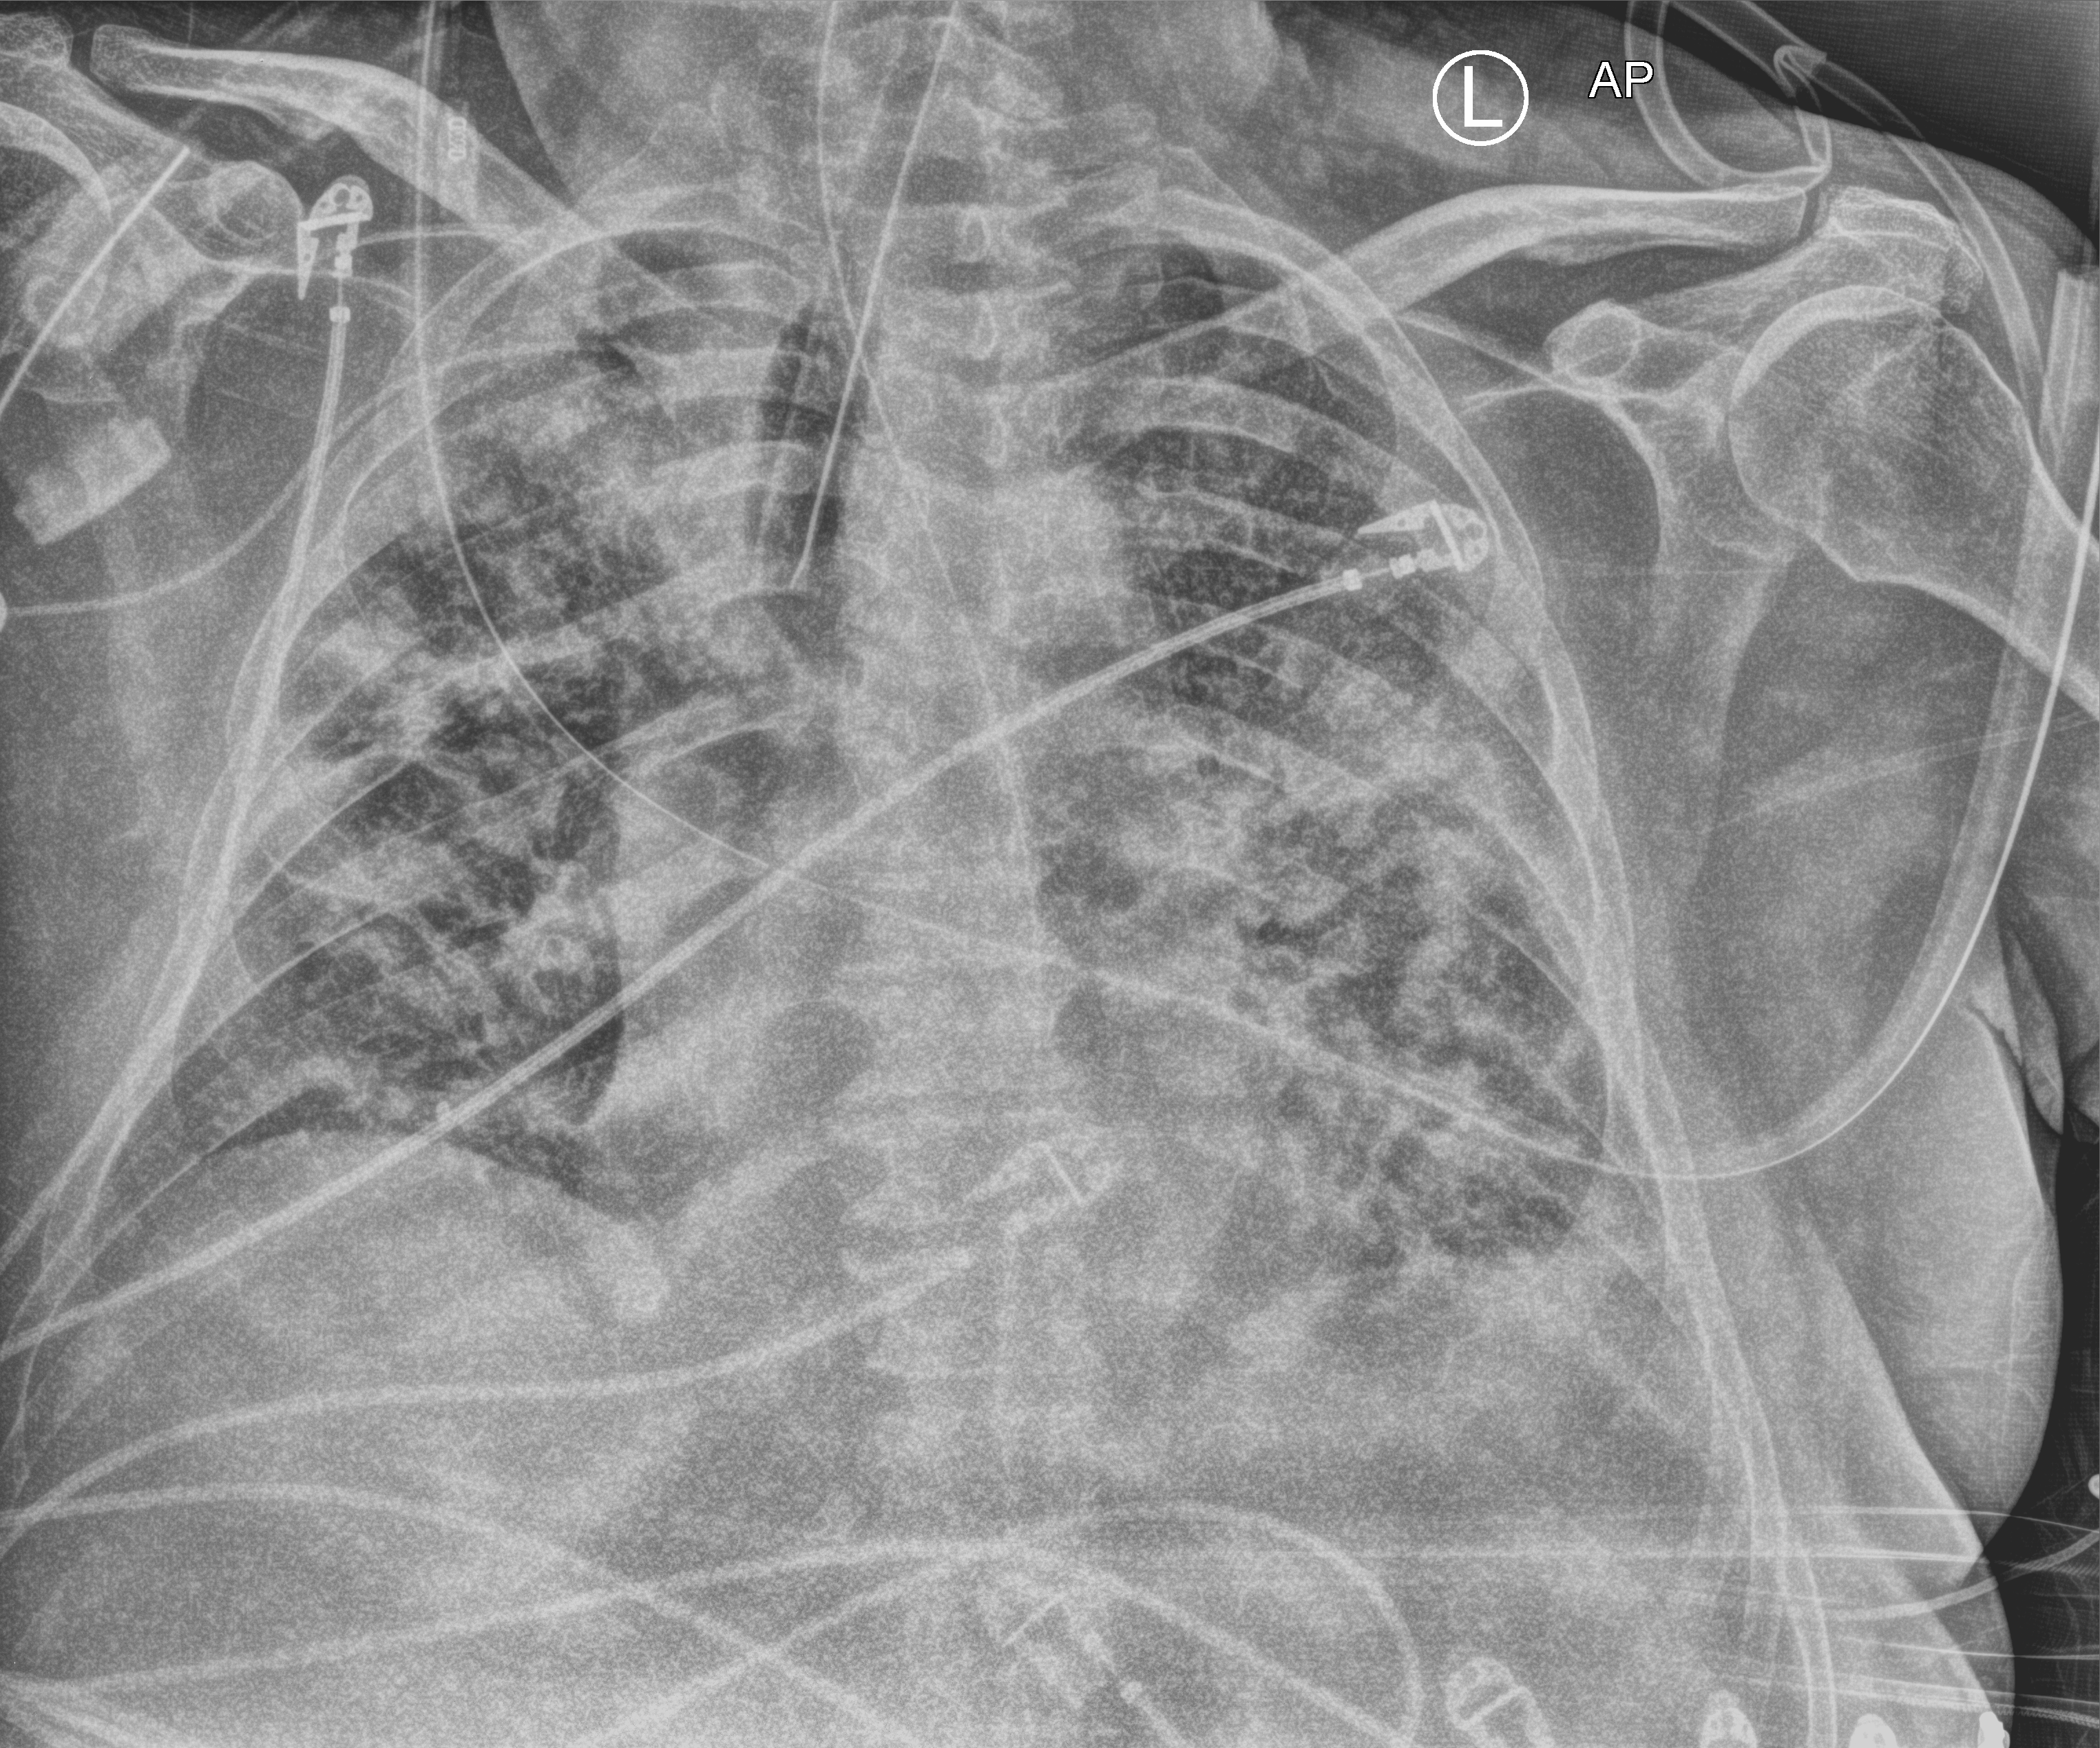
Portable chest radiograph. Patient hospitalised with COVID-19; male, aged 60–74 years.
Hospital-stay facts (about this admission, not read from this image; timing relative to this image not recorded):
- admitted to intensive care during this hospital stay: yes